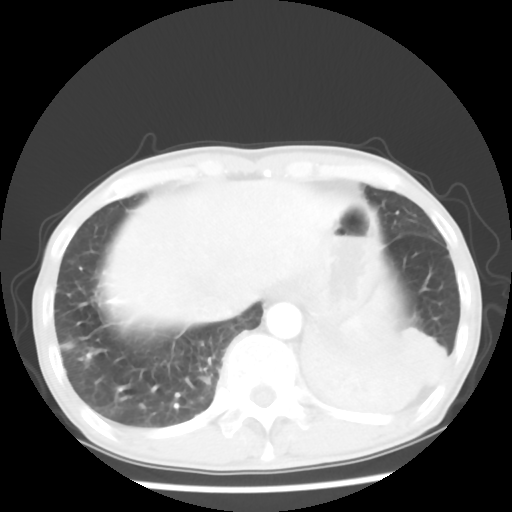
Chest CT, one axial slice. Position 12 of 64 along the scan axis. Reconstruction kernel STANDARD. 120 kVp. Lung window (W 1500 / L -600 HU). 512 × 512 image matrix. Male patient, age 68 years. From the clinical record (not read from this slice): clinical TNM (as recorded): T4 N0 M0.
Annotated regions visible in this slice (rectangle marked by the reading radiologist):
- lung tumour (recorded histology: squamous cell carcinoma): bounding box <288,298,460,437> (left, top, right, bottom; pixels)